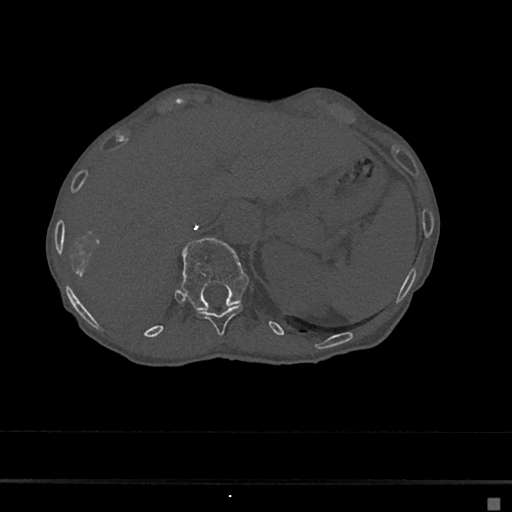
CT including the spine, one axial slice; slice 144 of 797 in the series (ordered by position); 120 kVp; bone window (W 1800 / L 400 HU); 0.5 mm slice thickness; 512 × 512 image matrix, field of view 360 × 360 mm. Female patient, age 68 years. Case-level facts recorded for this patient, not image findings: primary cancer: renal.
Annotated regions visible in this slice (semi-automatic segmentation, software-assisted and operator-edited):
- T11 vertebra: bounding box [x1, y1, x2, y2] px = [196, 304, 244, 335]
- T12 vertebra: [181, 238, 250, 311]